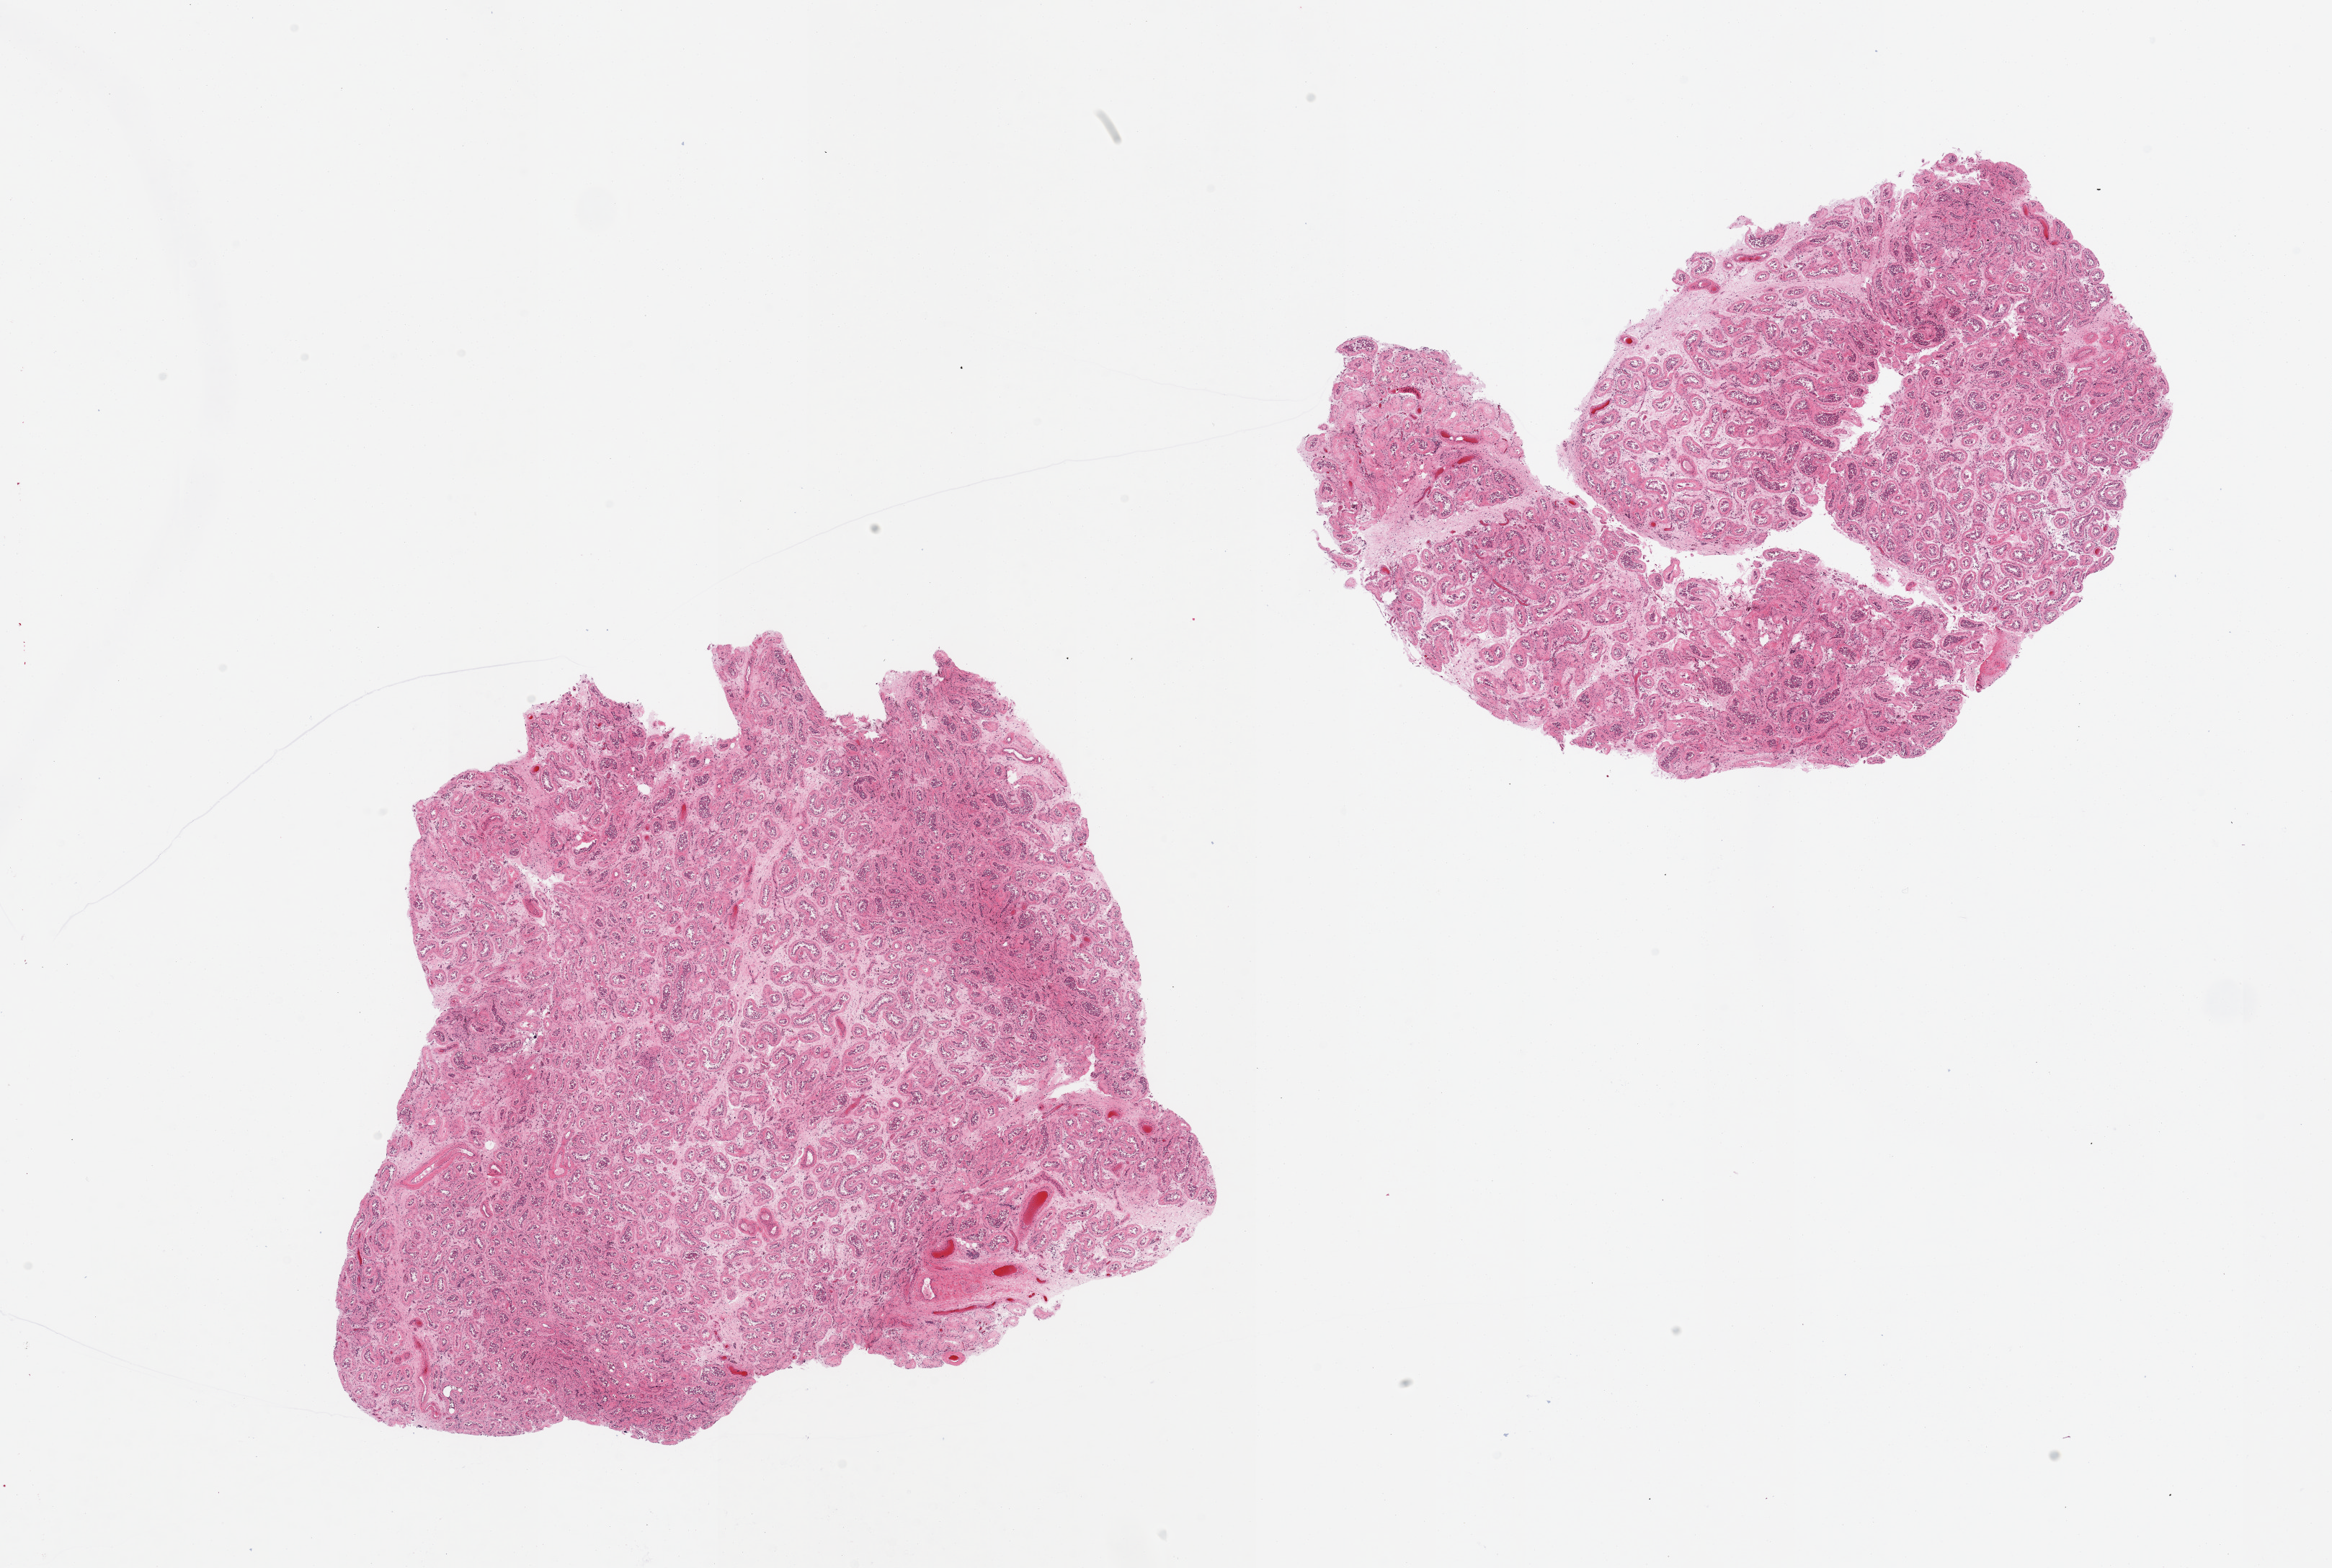
Whole-slide image, hematoxylin and eosin (H&E) stain, brightfield — a low-resolution overview of the entire scanned area, about 25.6 x 17.2 mm. PAXgene-fixed paraffin-embedded (PFPE) section. Section of testis (target tissue). Tissue donor sample. Donor sex: male.
Reviewer comment on this tissue sample: 2 pieces; thick tubular basement membrane; interstitial fibrosis; lack of spermatogenesis and increase of Sertolli cells.